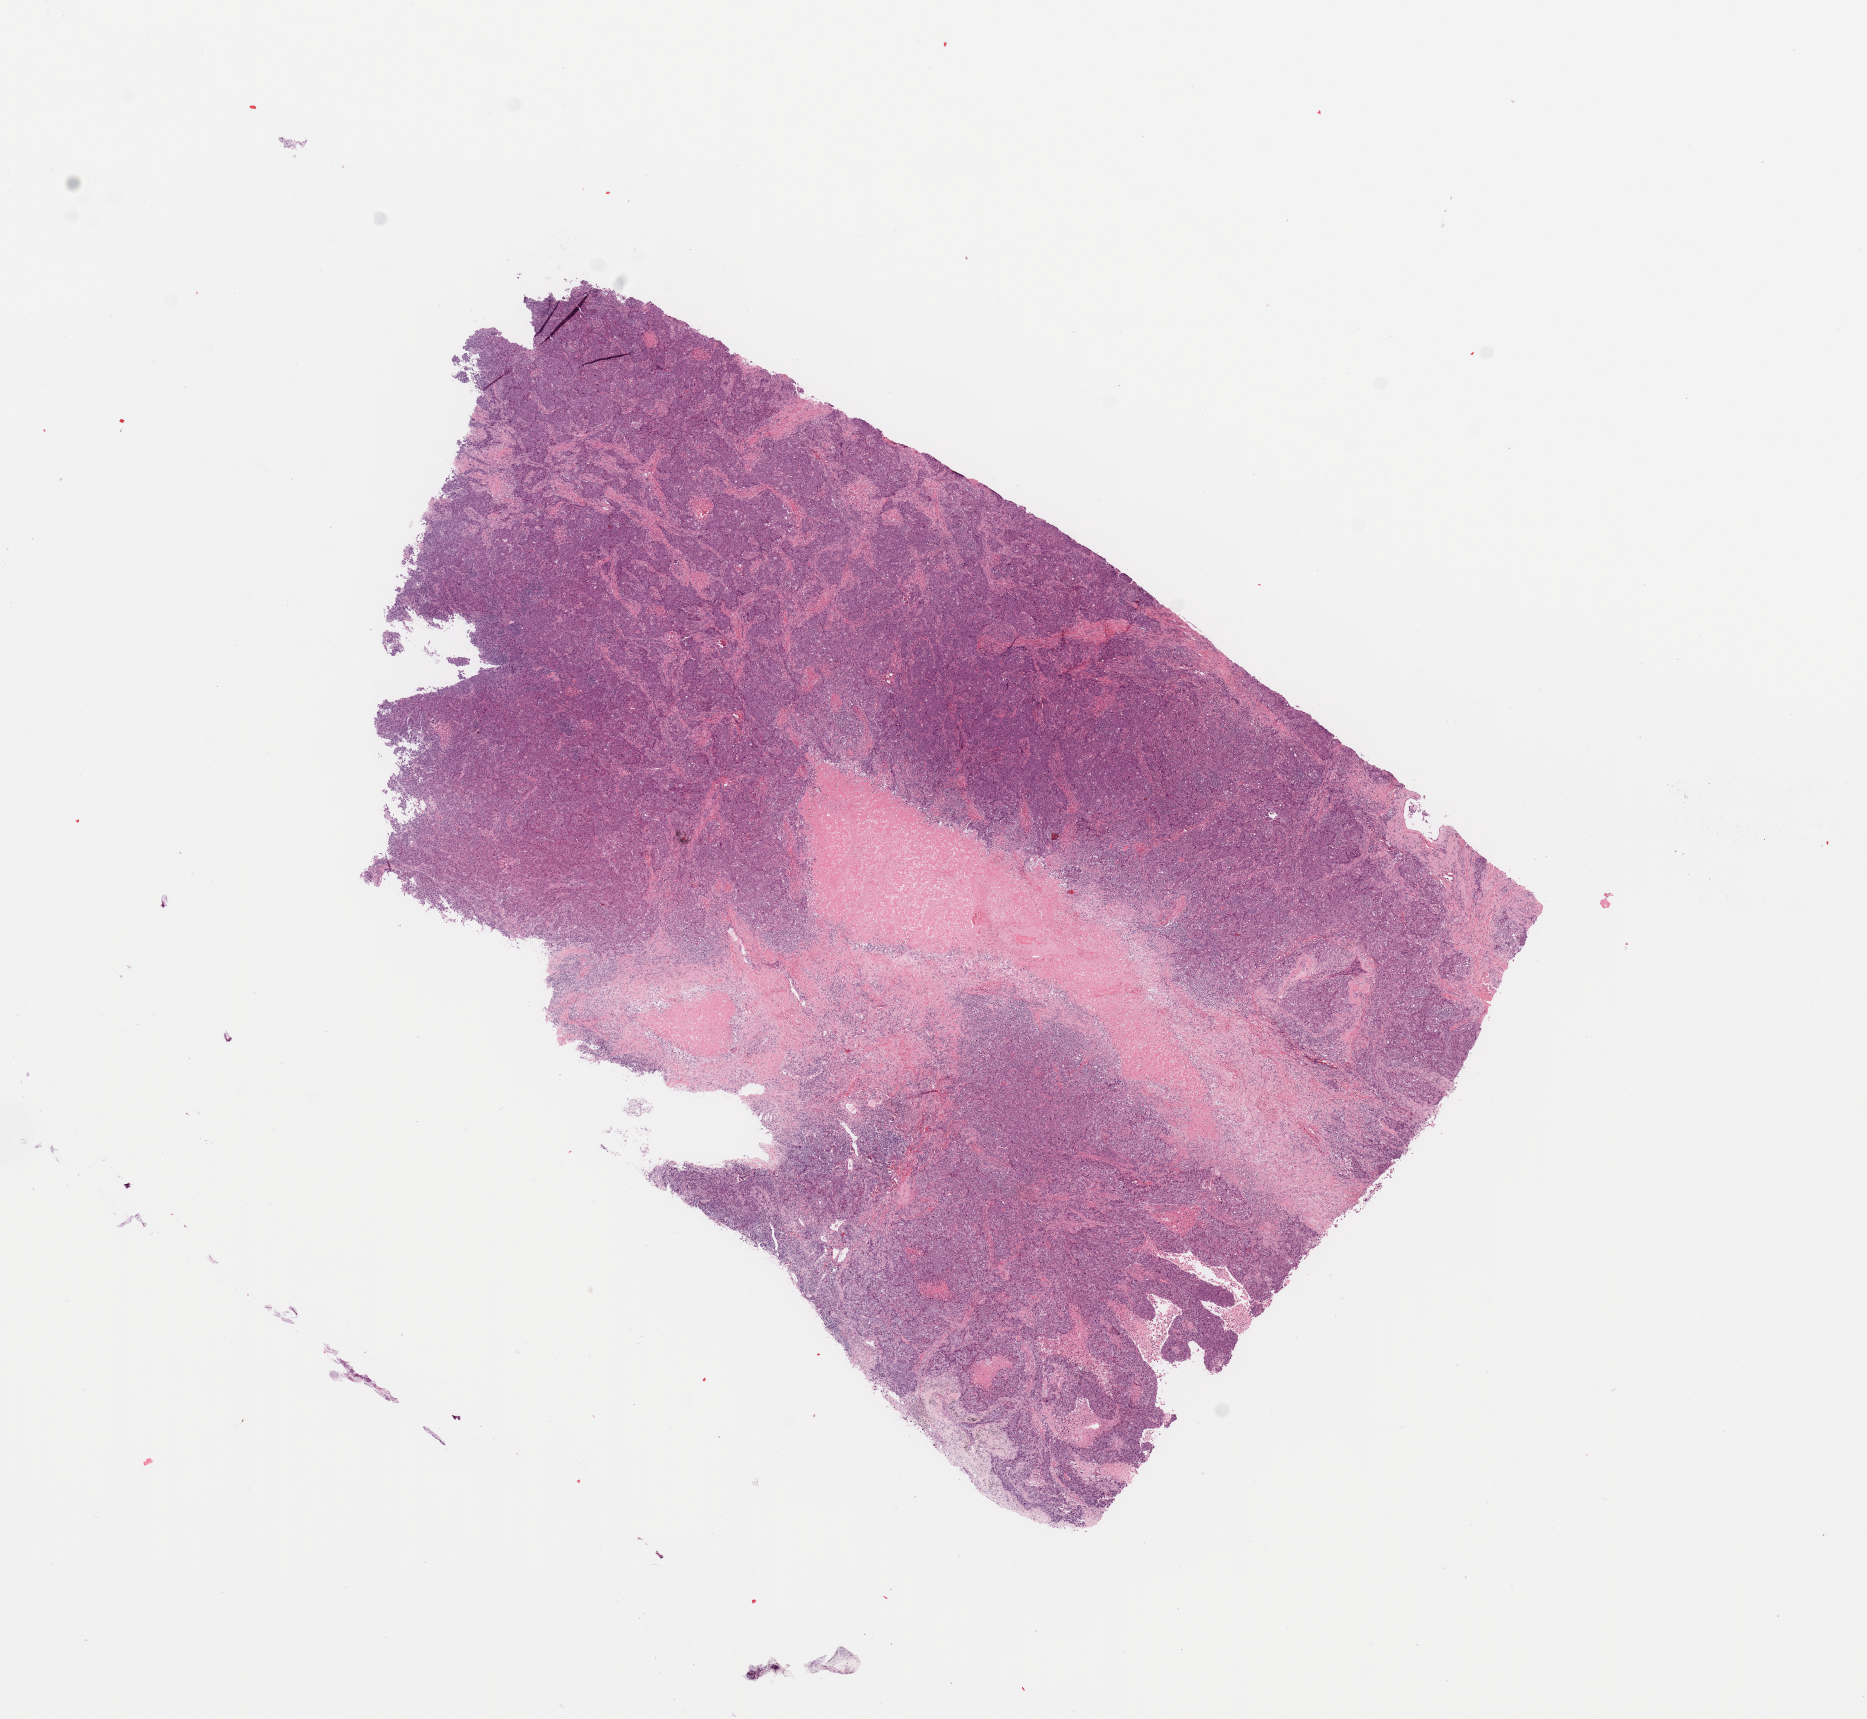
Whole-slide histology image, H&E — whole scanned area (about 14.8 x 13.6 mm, acquisition: 20x scan) shown as a low-resolution overview; lung, tumour tissue. 67-year-old male patient. Histologic grade: G3 (poorly differentiated).
Primary tumour site (as recorded): right lower lobe. AJCC pathologic stage: IIA. Histologic diagnosis: Adenocarcinoma, NOS.